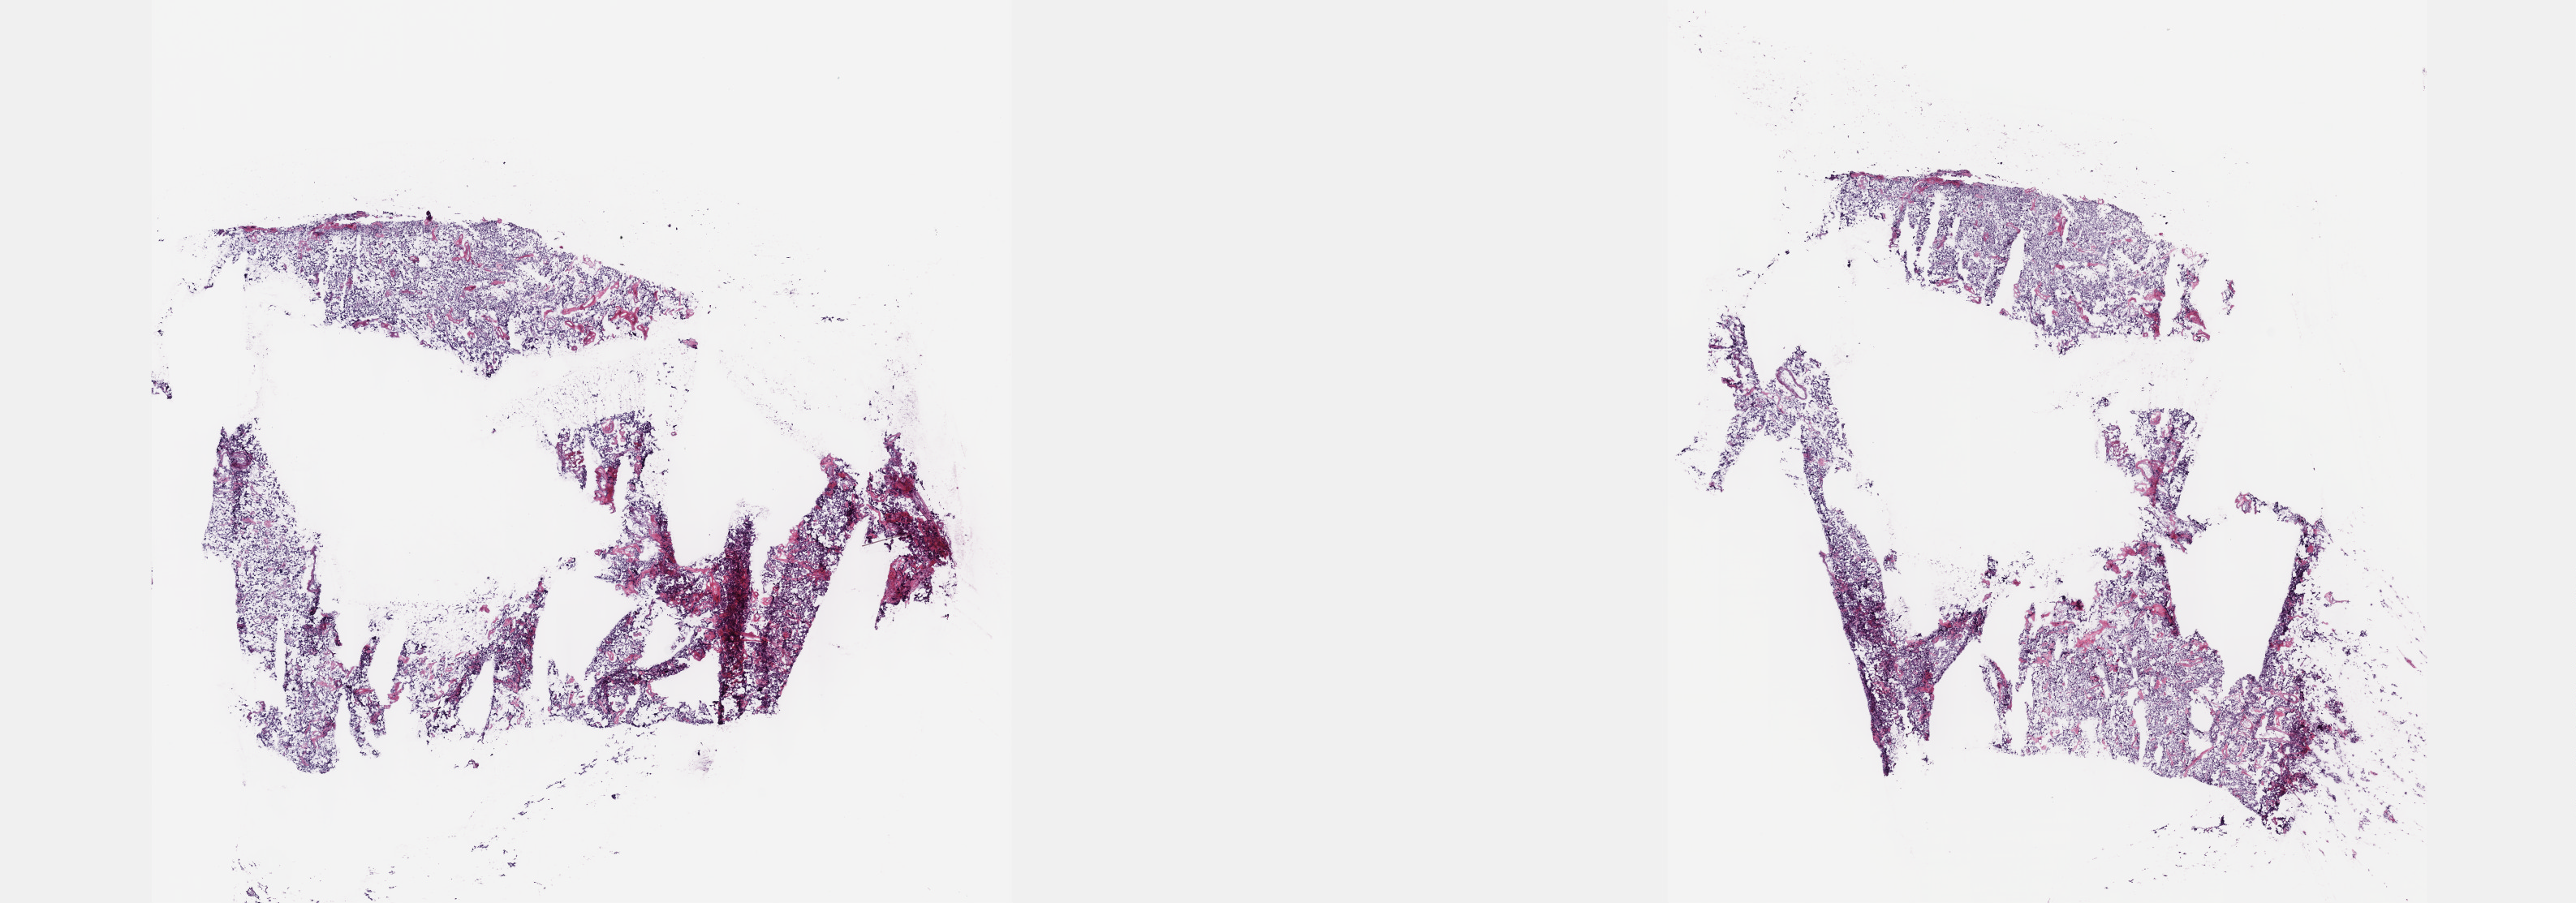
H&E whole-slide image, low-resolution overview of the scanned area, about 25.7 x 9.0 mm; frozen section from the top of the tissue portion; sample: primary tumour, adrenal gland. Patient: male, age at initial diagnosis 59 years. Composition of this section per pathologist review: tumour cells 95%, tumour nuclei 99%, normal cells 0%, stromal cells 5%, necrosis 0%. Inflammatory infiltration, as recorded: lymphocyte infiltration 0%, monocyte infiltration 0%, neutrophil infiltration 0%.
Pathologic diagnosis: Pheochromocytoma, malignant.